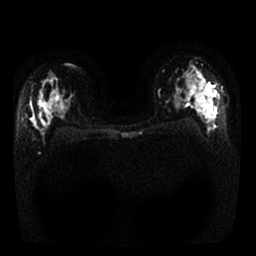
Breast MRI, one axial slice; position 16 of 25 along the scan axis; diffusion-weighted series; image 2 of 4 stored at this slice position (different b-values; order by instance number); 1.5 T; 4 mm slice thickness; 256 × 256 image matrix. Female patient.
Outlined on this slice (expert manual segmentation):
- tumour on diffusion-weighted imaging: bounding box [x1, y1, x2, y2] px = [196, 76, 217, 97]